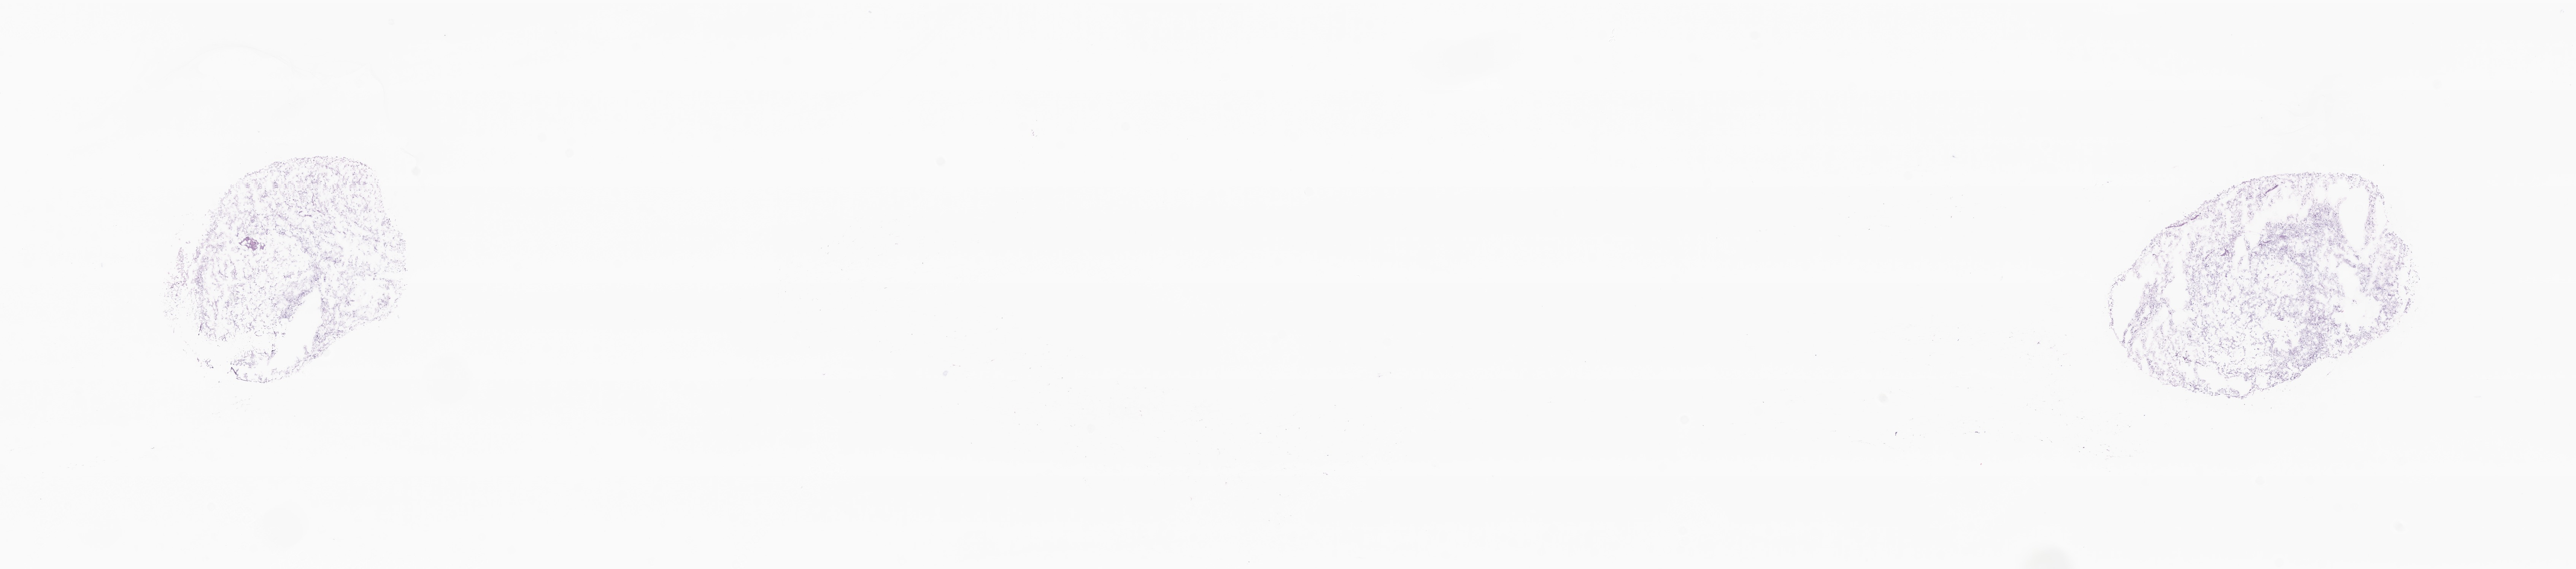
Whole-slide image, haematoxylin and eosin stain of tumor tissue from the brain — low-resolution overview of the scanned area, about 28.6 x 6.3 mm, cryosection (OCT / tissue freezing medium). Patient female; age 83 months (6 years 11 months).
Diagnosis (ICD-O-3 morphology term): Dysembryoplastic neuroepithelial tumor.